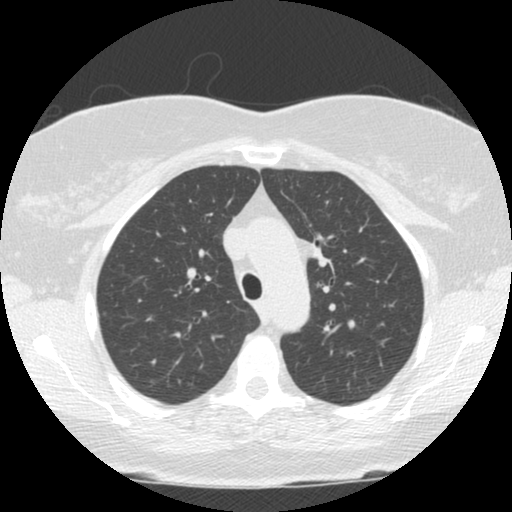
Axial slice from a low-dose chest CT screening exam, second annual screen, lung window (W 1500 / L -600 HU), 2.5 mm slice thickness, 120 kVp, slice 37 of 120 in the series, 512 × 512 image matrix, field of view 310 × 310 mm. Female, age 66 years at enrolment. Former smoker at enrolment.
- Expert reader's lesion annotation, bounding box [x1, y1, x2, y2] px = [287, 231, 346, 278].
- Screening reader's record for this exam (one nodule recorded; not confirmed to be the boxed lesion): non-calcified nodule or mass ≥4 mm, left upper lobe, 12 × 9 mm, smooth margins, soft tissue attenuation, pre-existing on the prior screen: no.
- Later outcome: lung cancer diagnosed 196 days after this screen — small cell carcinoma, NOS, left upper lobe, stage IIIA (AJCC 6th edition), 50 mm at pathology.